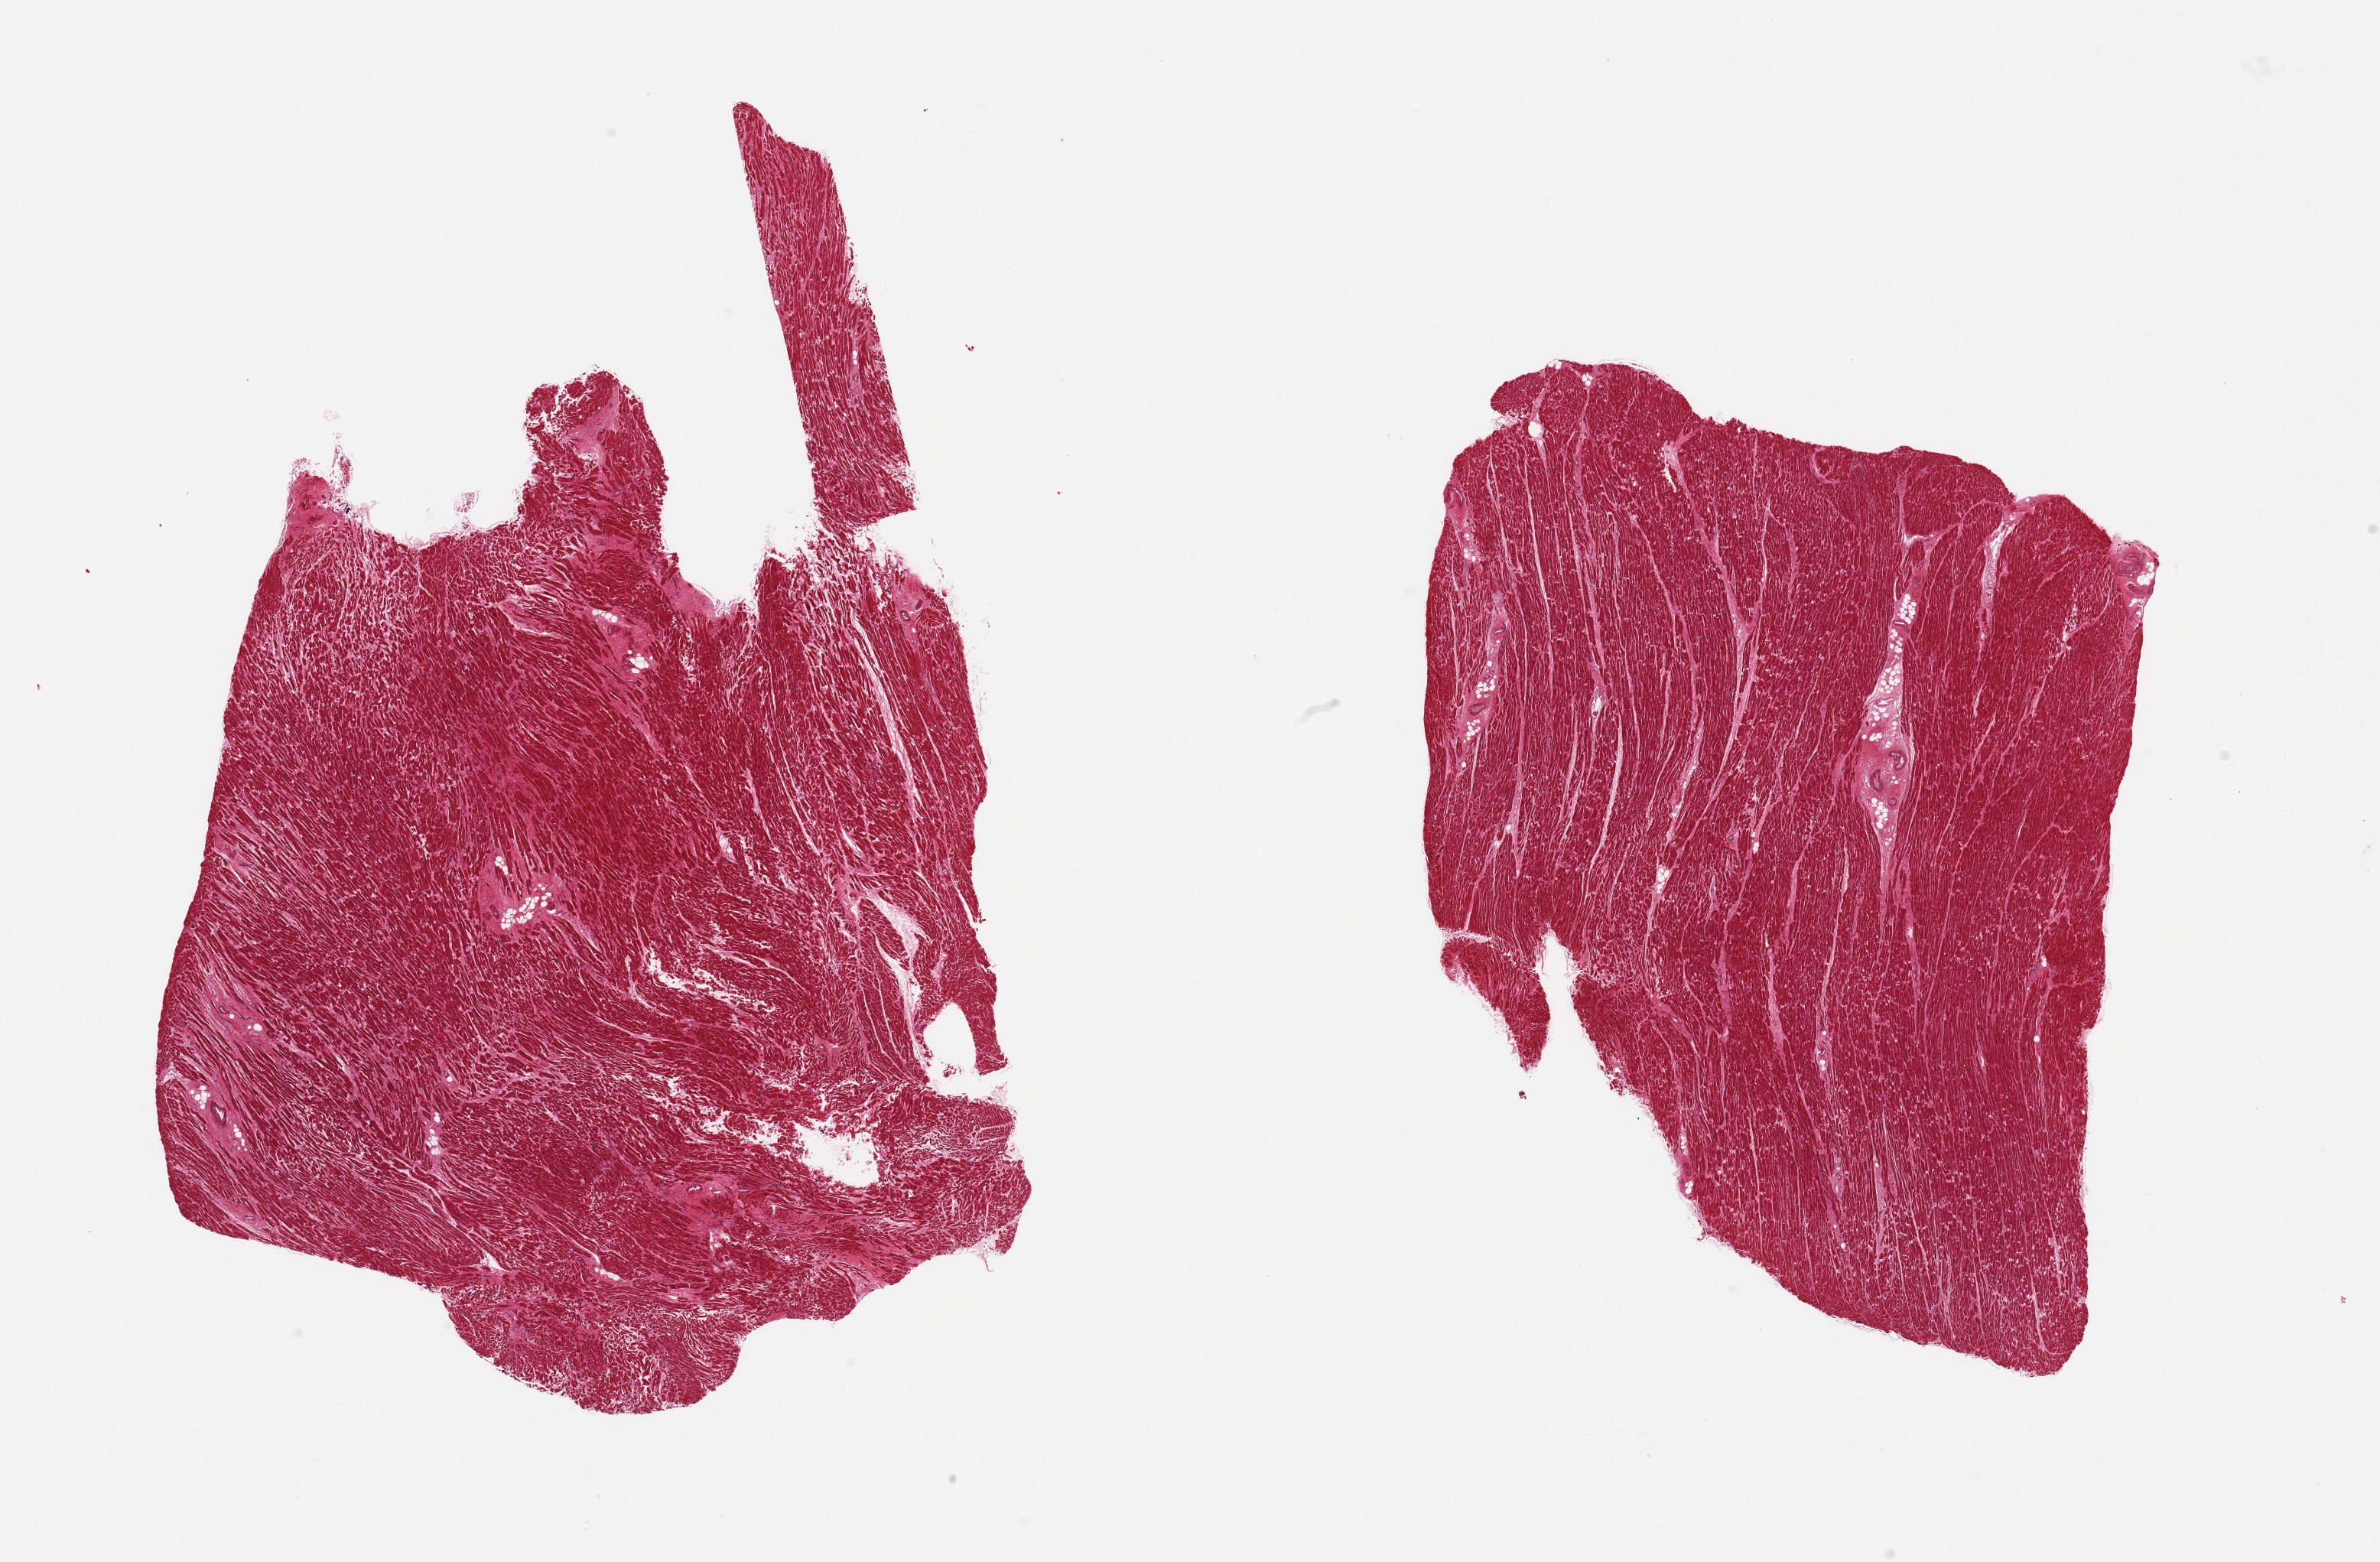
Digitized haematoxylin and eosin-stained section, shown as a low-resolution overview of the whole scanned area (about 24.6 x 16.1 mm), PAXgene-fixed paraffin-embedded (PFPE) section, target tissue: heart, tissue donor sample. Male donor.
Pathologist's review note for this sample: 2 pieces; patchy interstitial fibrosis, myocyte hypertrophy.